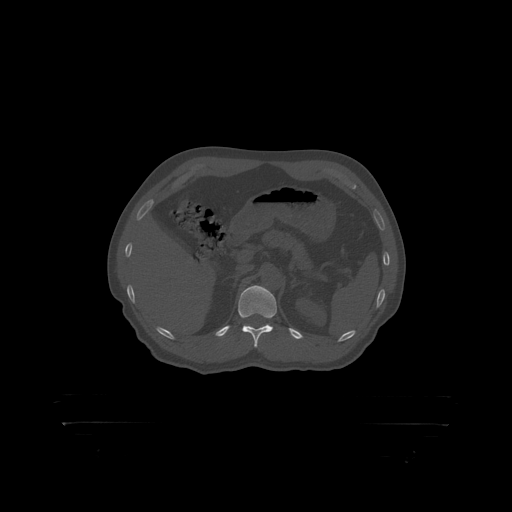
CT including the spine, one axial slice. Position 348 of 399 along the scan axis. 120 kVp. Bone window (W 1800 / L 400 HU). 512 × 512 image matrix, field of view 650 × 650 mm. Male patient, age 46 years. Case-level facts recorded for this patient, not image findings: primary cancer: skin.
Annotated regions visible in this slice (semi-automatic segmentation, software-assisted and operator-edited):
- T12 vertebra: bounding box <238,286,277,318> (left, top, right, bottom; pixels)